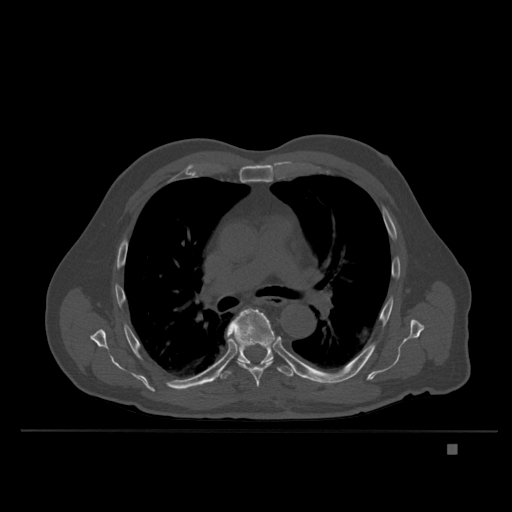
CT including the spine, one axial slice; slice 253 of 435 in the series (ordered by position); bone window (W 1800 / L 400 HU); 512 × 512 image matrix. Patient: male, 73 years. Case-level facts recorded for this patient, not image findings: primary cancer: skin.
Annotated regions visible in this slice (semi-automatic segmentation, software-assisted and operator-edited):
- T6 vertebra: bounding box (x1, y1, x2, y2) in pixels: (226, 308, 275, 388)
- T7 vertebra: (210, 340, 301, 383)